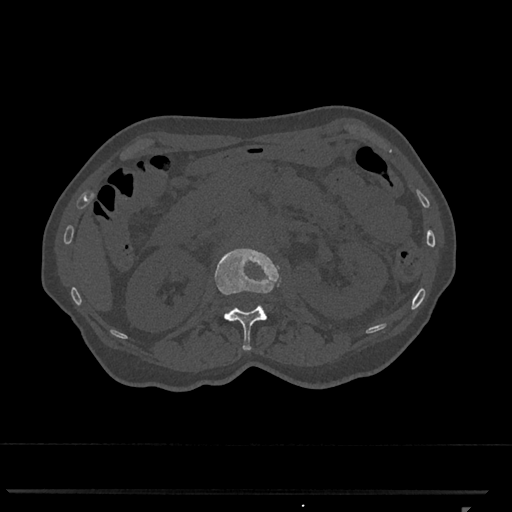
CT including the spine, one axial slice. Slice 390 of 793 in the series (ordered by position). 120 kVp. Bone window (W 1800 / L 400 HU). 0.5 mm slice thickness. 512 × 512 image matrix, field of view 380 × 380 mm. Female patient, age 62 years. Case-level facts recorded for this patient, not image findings: primary cancer: renal.
Structures marked on this image (semi-automatically segmented with operator editing):
- L1 vertebra: bounding box [x1, y1, x2, y2] px = [214, 248, 281, 351]